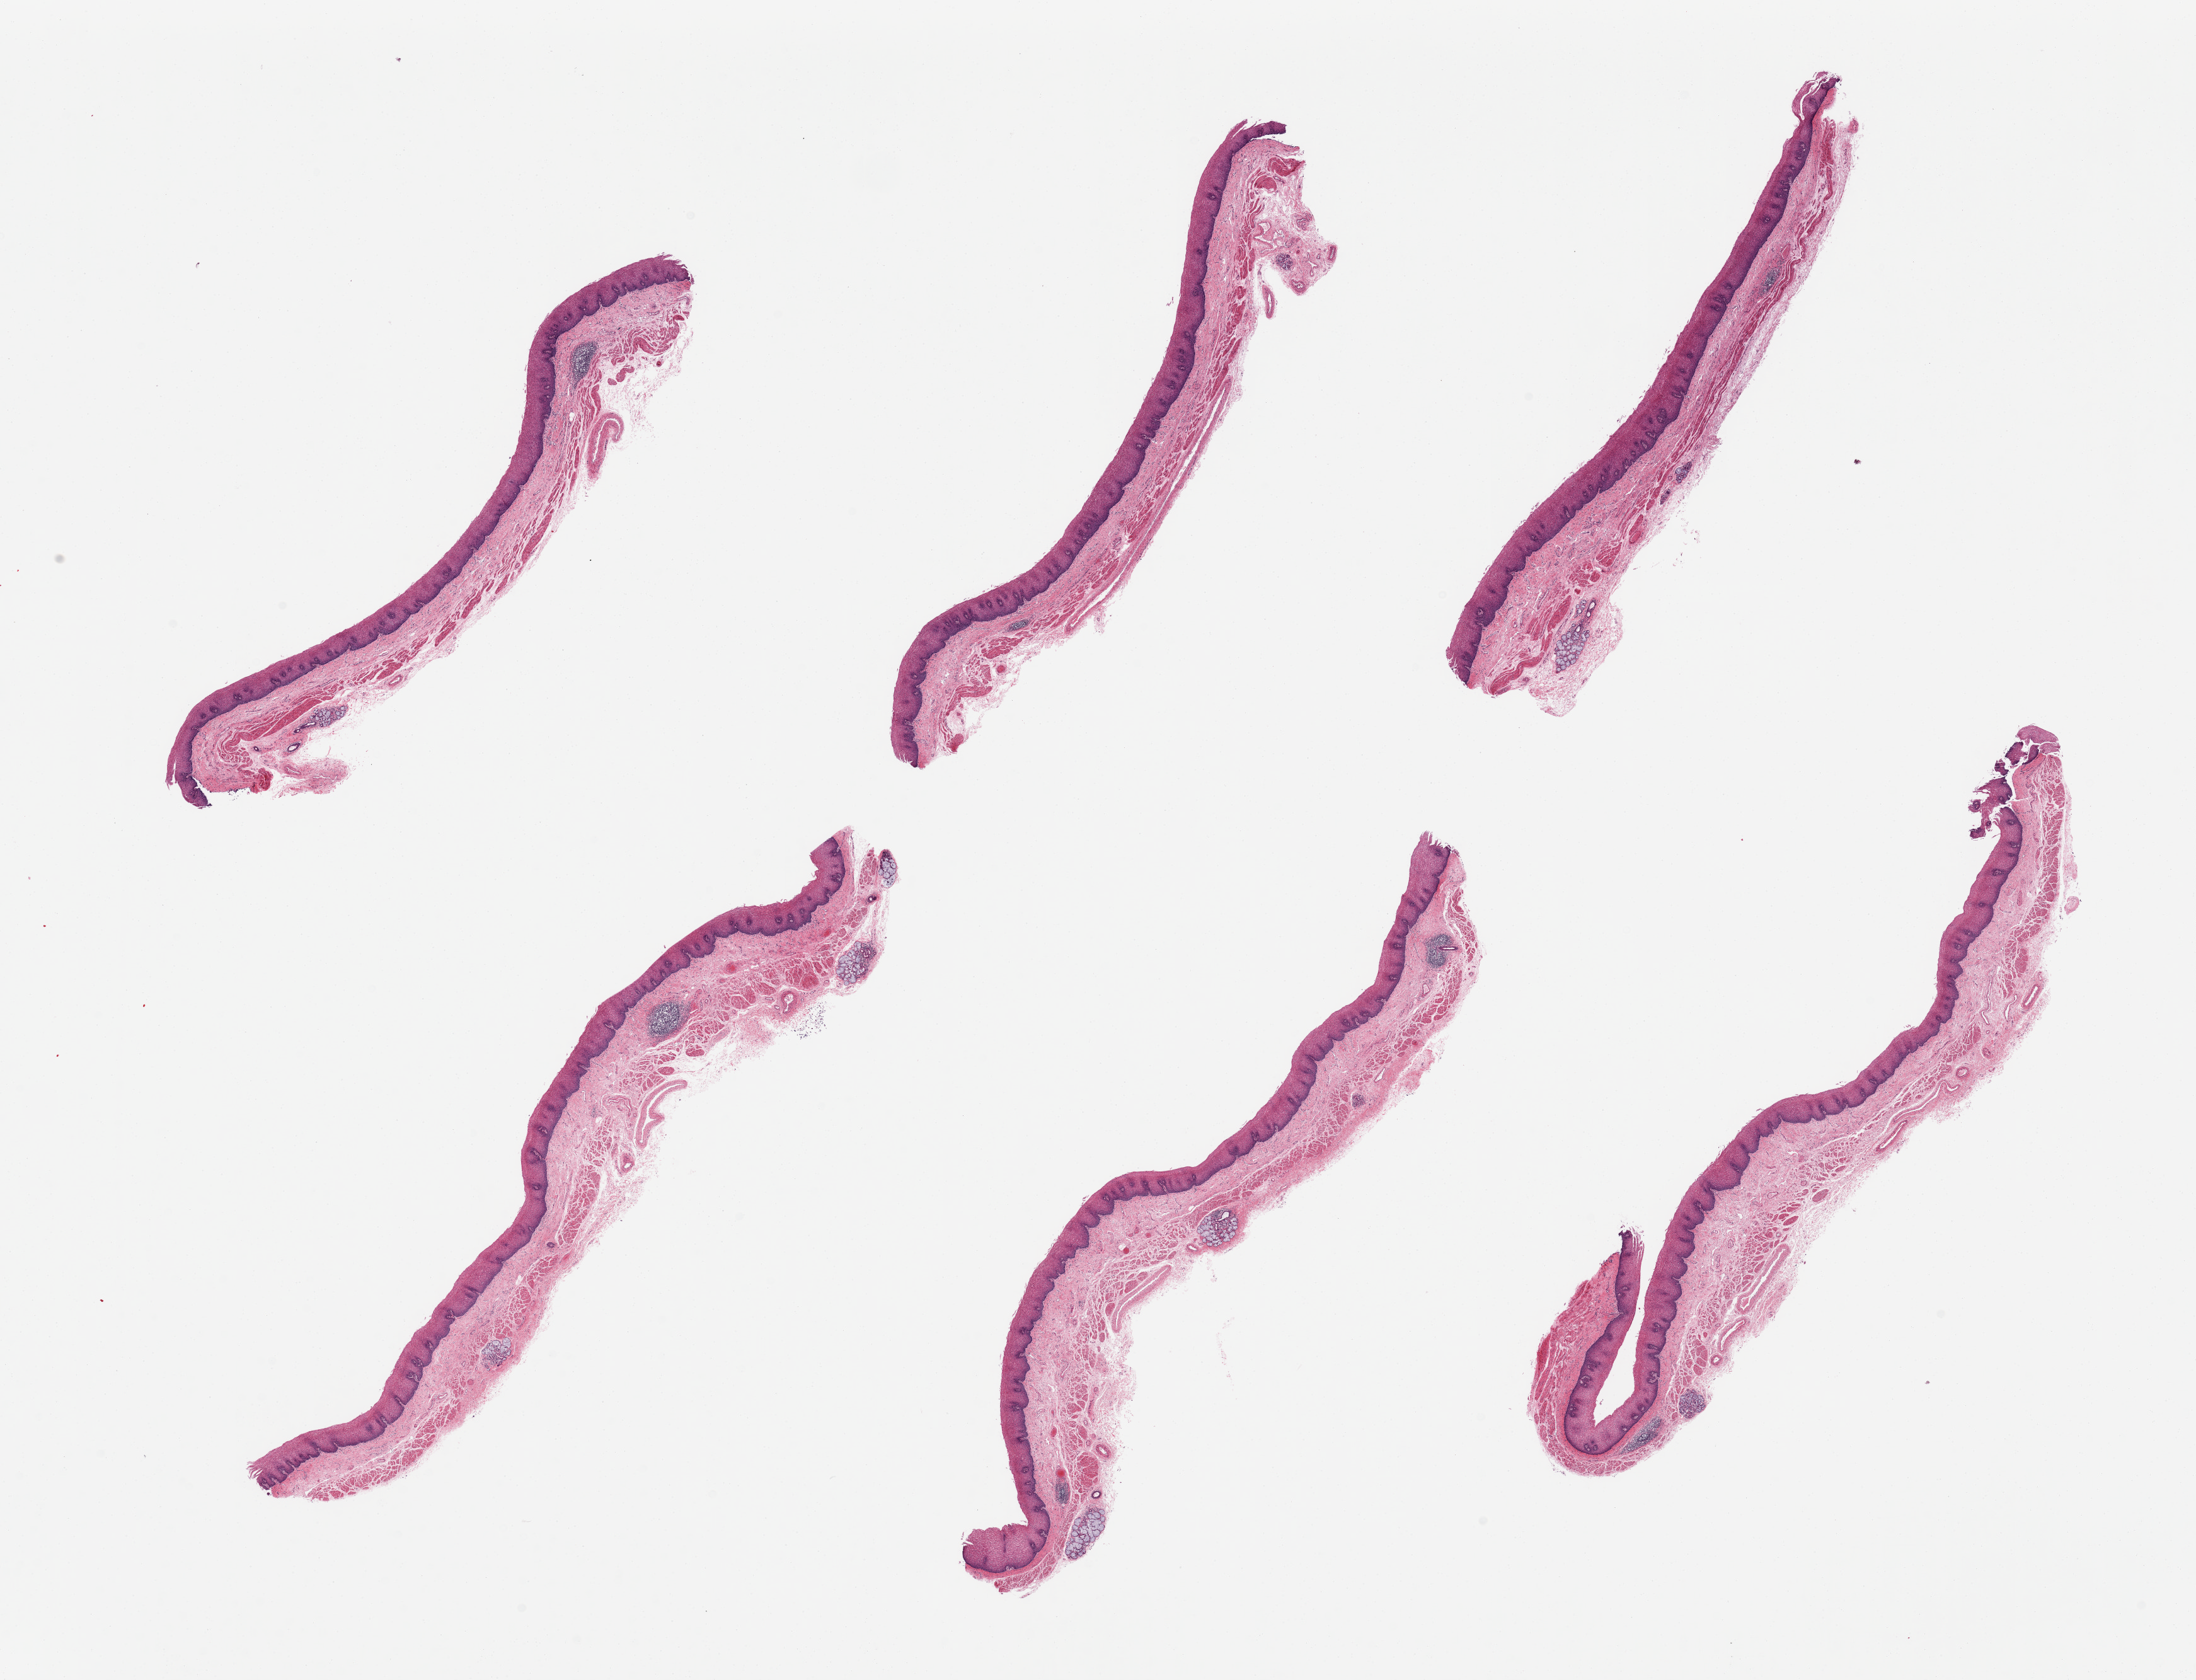
H&E whole-slide image — low-resolution overview of the scanned area, about 27.6 x 21.1 mm (acquisition: 20x scan), PAXgene-fixed paraffin-embedded (PFPE) section, target tissue: esophageal mucous membrane, tissue donor sample.
* review note (as recorded): 6 pieces, few clusters of submucosal glands